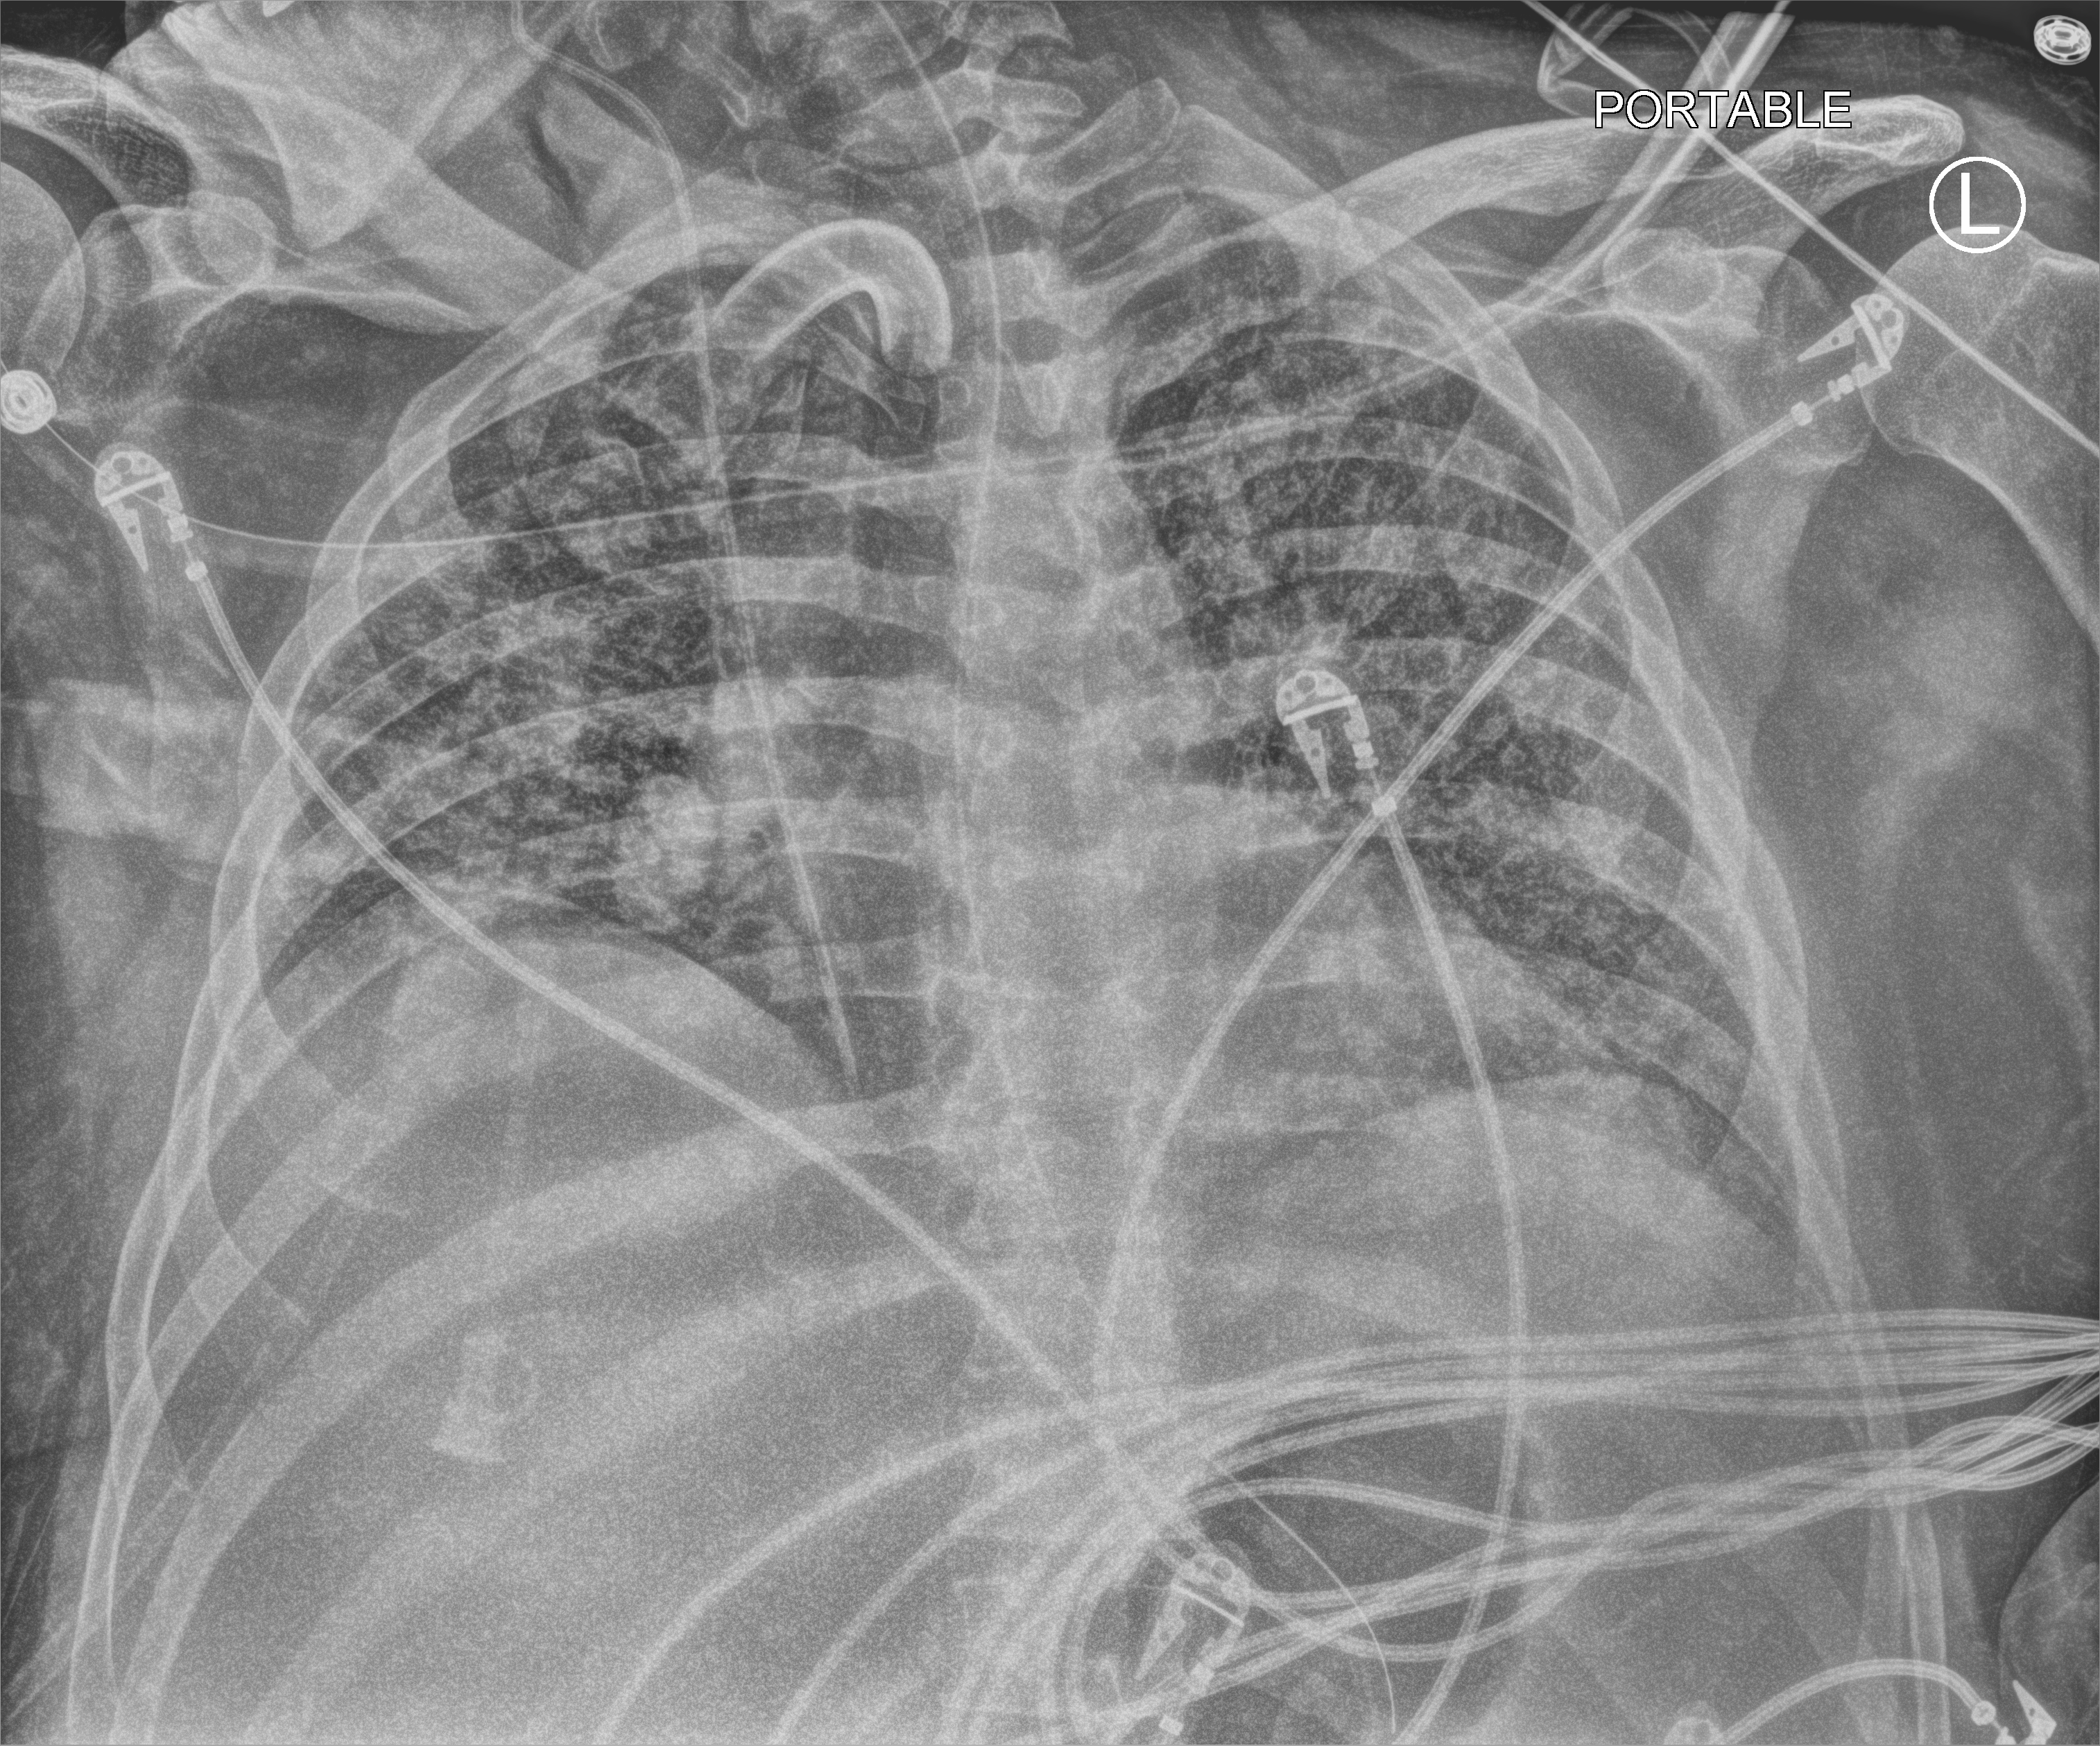
Portable chest radiograph. Patient hospitalised with COVID-19; male, aged 18–59 years.
Hospital-stay facts (about this admission, not read from this image; timing relative to this image not recorded):
- mechanically ventilated during this hospital stay: yes
- admitted to intensive care during this hospital stay: yes
- smoking status (admission record): never